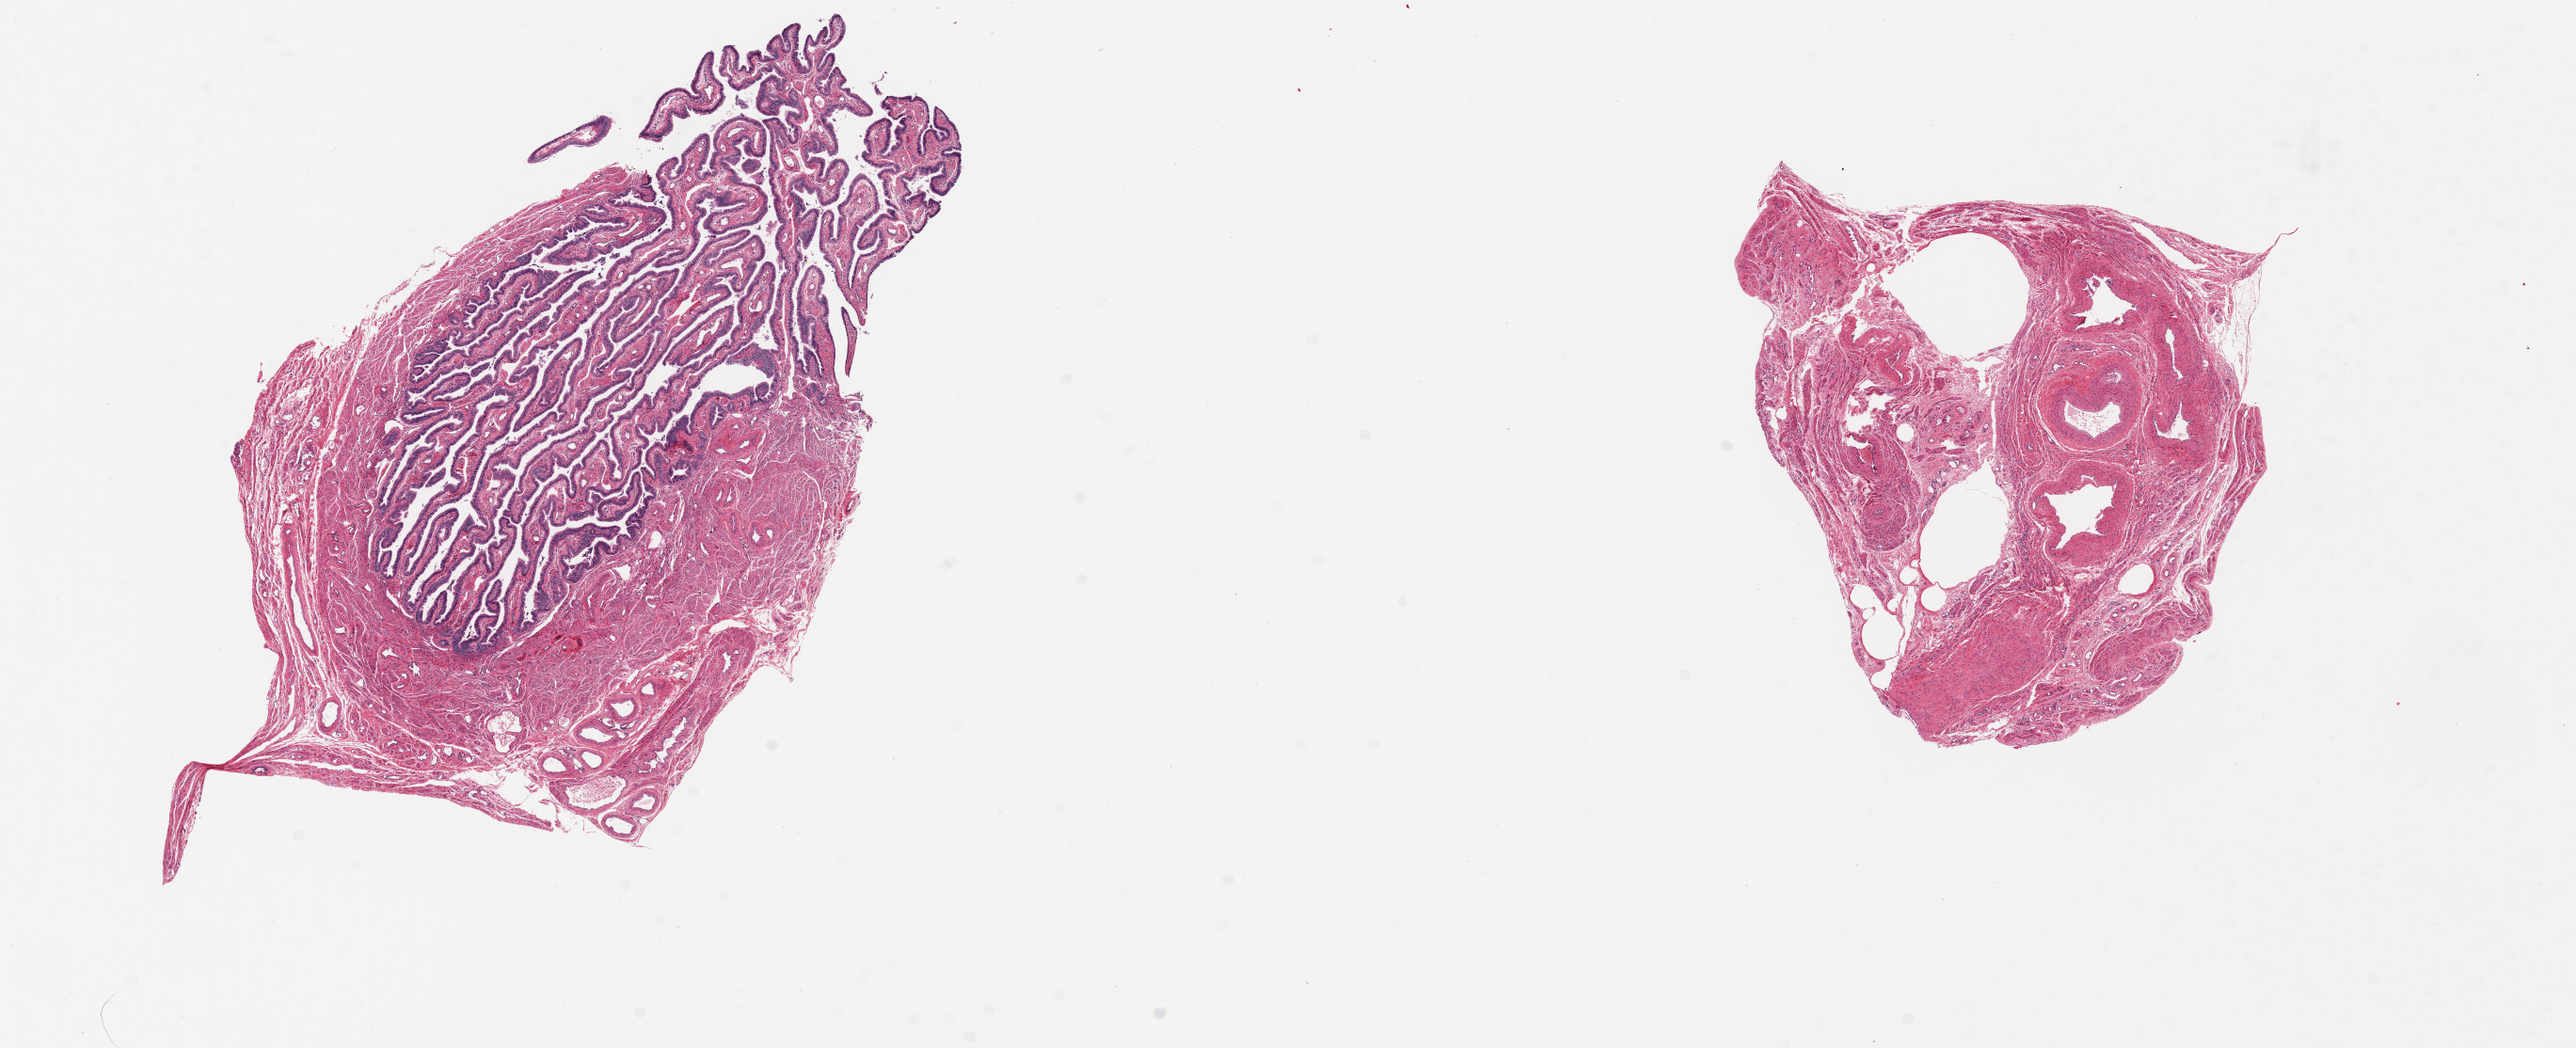
Haematoxylin and eosin whole-slide image, shown as a low-resolution overview of the whole scanned area (about 21.7 x 8.8 mm); PAXgene-fixed paraffin-embedded (PFPE) section; sampled site (target tissue): fallopian tube; tissue donor sample.
* reviewer comment on this tissue sample: 2 pieces 8x5 & 4x4 mm; larger piece is good tube, smaller is fibrovascular tissue with no tubal elements